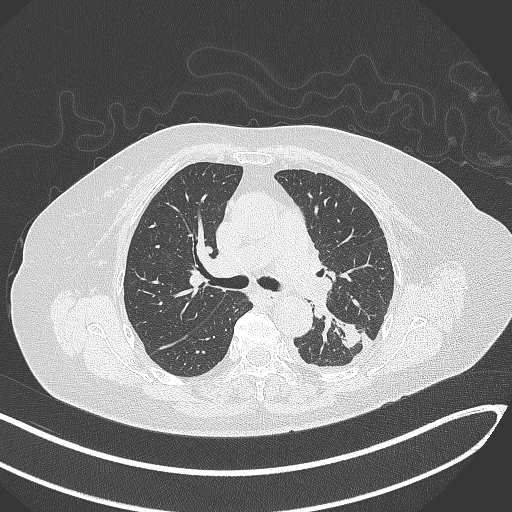
Chest CT, one axial slice. Slice 198 of 270 in the series (ordered by position). Reconstruction kernel B70f. 120 kVp. Lung window (W 1500 / L -600 HU). 512 × 512 image matrix. Patient: female, 76 years. Case-level facts recorded for this patient, not image findings: clinical TNM (as recorded): T1c N0 M0.
Structures marked on this image (bounding box drawn by a radiologist):
- lung tumour (recorded histology: adenocarcinoma): bounding box (x1, y1, x2, y2) in pixels: (333, 321, 369, 353)